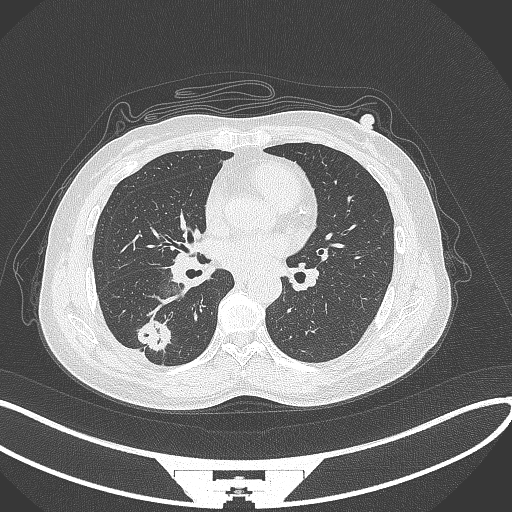
Chest CT, one axial slice; position 144 of 352 along the scan axis; reconstruction kernel B70f; lung window (W 1500 / L -600 HU); 1 mm slice thickness; 512 × 512 image matrix, field of view 400 × 400 mm. Female patient, age 55 years. Case-level facts recorded for this patient, not image findings: clinical TNM (as recorded): T1c N1 M0.
Structures marked on this image (rectangle marked by the reading radiologist):
- lung tumour (recorded histology: adenocarcinoma): bounding box [x1, y1, x2, y2] px = [136, 318, 174, 357]